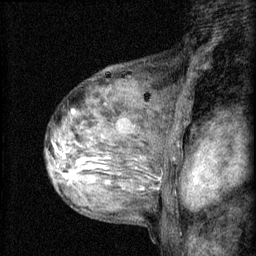
Breast MRI (dynamic contrast-enhanced), one sagittal slice. Position 42 of 60 along the scan axis. 3 images stored at this slice position (order not interpretable as contrast timing). 1.5 T. TE 4.2 ms, TR 8.2 ms. 2 mm slice thickness. 256 × 256 image matrix, field of view 180 × 180 mm. Female patient, age 48 years.
Annotated regions visible in this slice (semi-automatically segmented with operator editing):
- analysis volume of interest (the breast-tissue region the enhancement analysis was run in; not a lesion): bounding box (x1, y1, x2, y2) in pixels: (54, 138, 133, 191)
- tumour enhancement mask (voxels above the 70 % enhancement threshold inside the analysis volume of interest): (54, 144, 109, 185)